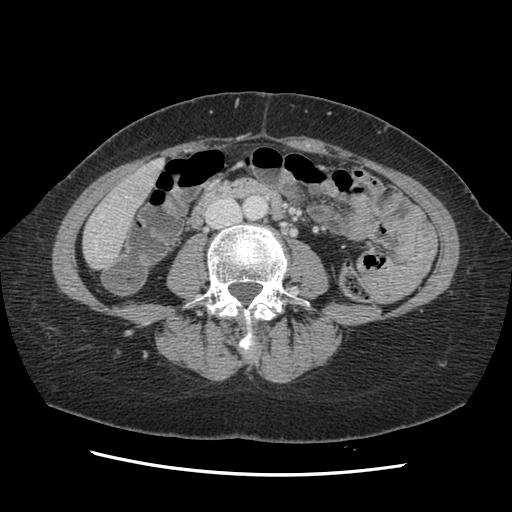
Contrast-enhanced abdominal CT, one axial slice. Position 28 of 141 along the scan axis. 120 kVp. Soft-tissue window (W 400 / L 40 HU). 512 × 512 image matrix. Female patient, age 61 years. From the clinical record (not read from this slice): diagnosis: colorectal cancer liver metastases, imaged before liver resection; multiple liver metastases: no; largest metastasis: 2.4 cm.
Outlined on this slice (expert manual segmentation):
- hepatic veins: bounding box [x1, y1, x2, y2] px = [95, 173, 151, 251]
- liver: [84, 161, 163, 269]
- planned liver remnant (the part of the liver to remain after resection): [84, 162, 163, 269]